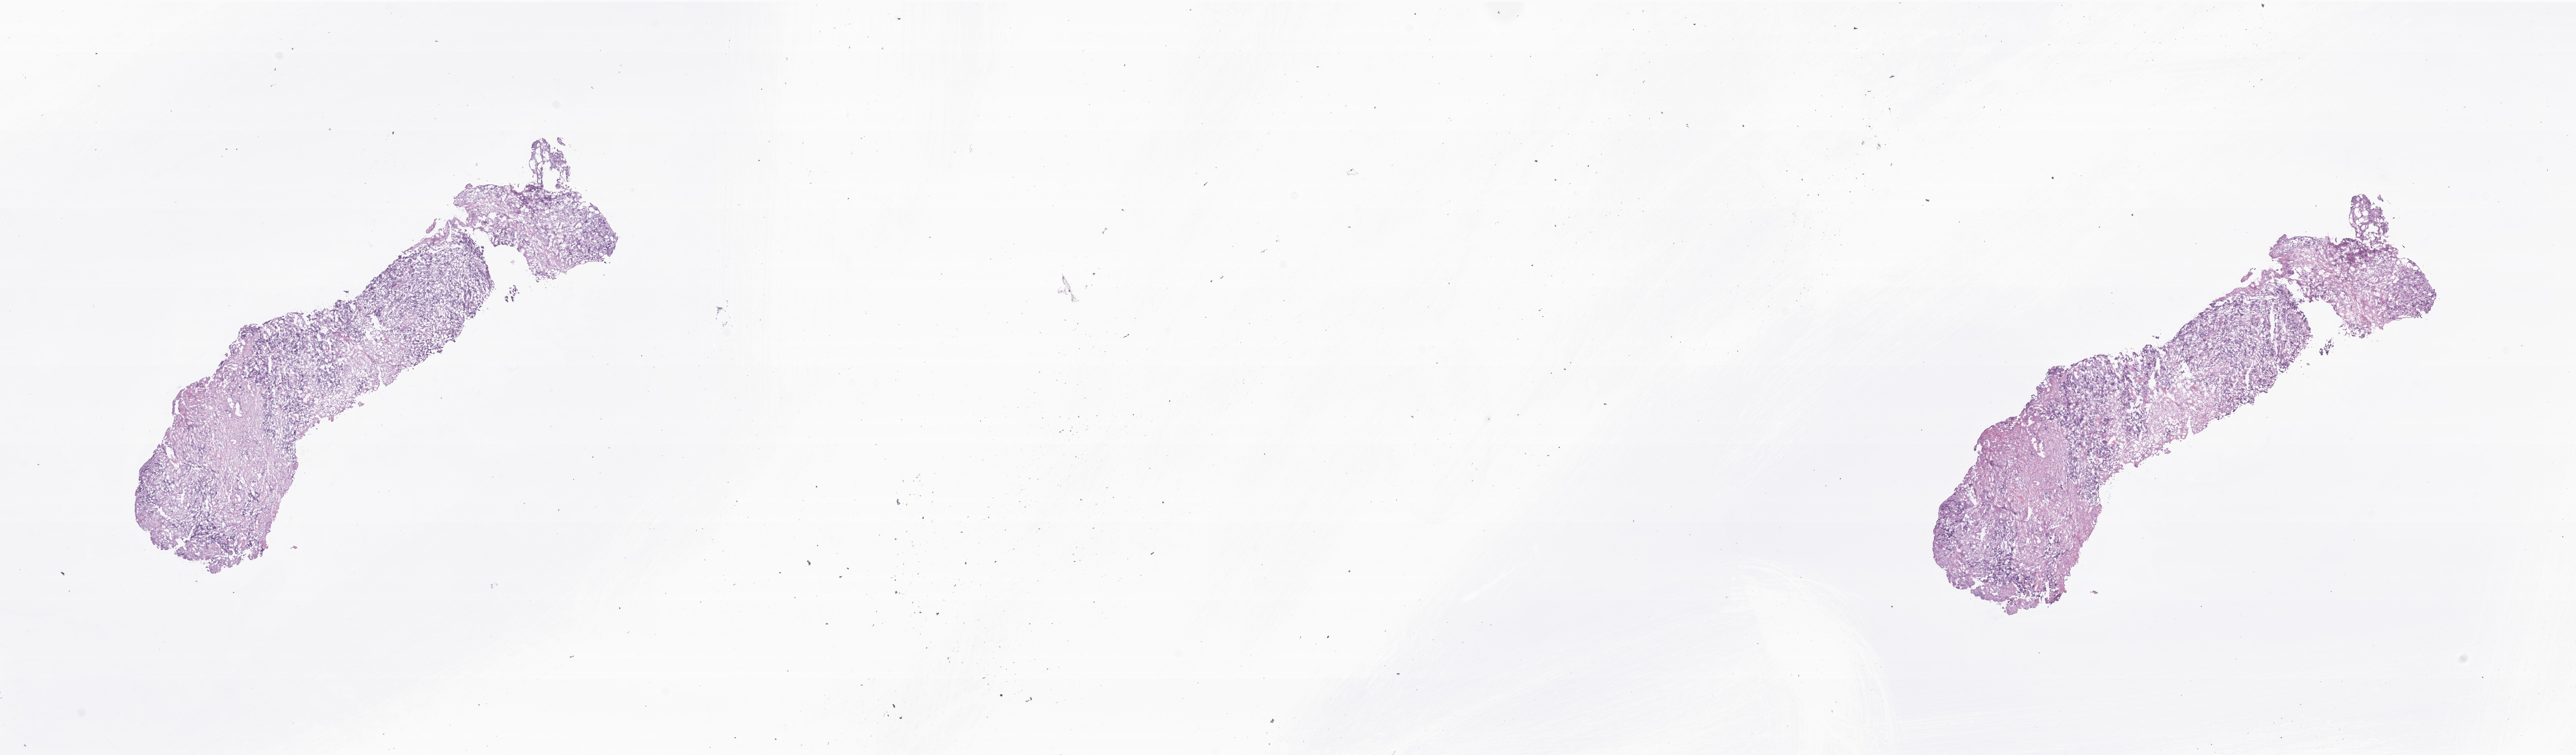
H&E whole-slide image of tumor tissue from the soft tissue of trunk, shown as a low-resolution overview of the whole scanned area (about 35.1 x 10.3 mm). Cryosection (OCT / tissue freezing medium). Patient: female, age 179 months (14 years 11 months).
Recorded diagnosis: Alveolar rhabdomyosarcoma. Tissue or organ of origin (case record): connective, subcutaneous and other soft tissues of trunk.